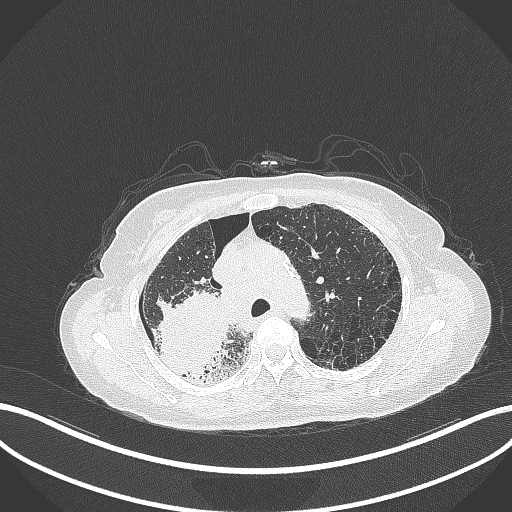
Chest CT, one axial slice; reconstruction kernel B70f; 120 kVp; lung window (W 1500 / L -600 HU); 1 mm slice thickness; 512 × 512 image matrix, field of view 400 × 400 mm. Patient: female, 64 years. Case-level facts recorded for this patient, not image findings: clinical TNM (as recorded): T3 N3 M0.
Outlined on this slice (bounding box drawn by a radiologist):
- lung tumour (recorded histology: squamous cell carcinoma): bounding box <146,286,230,381> (left, top, right, bottom; pixels)